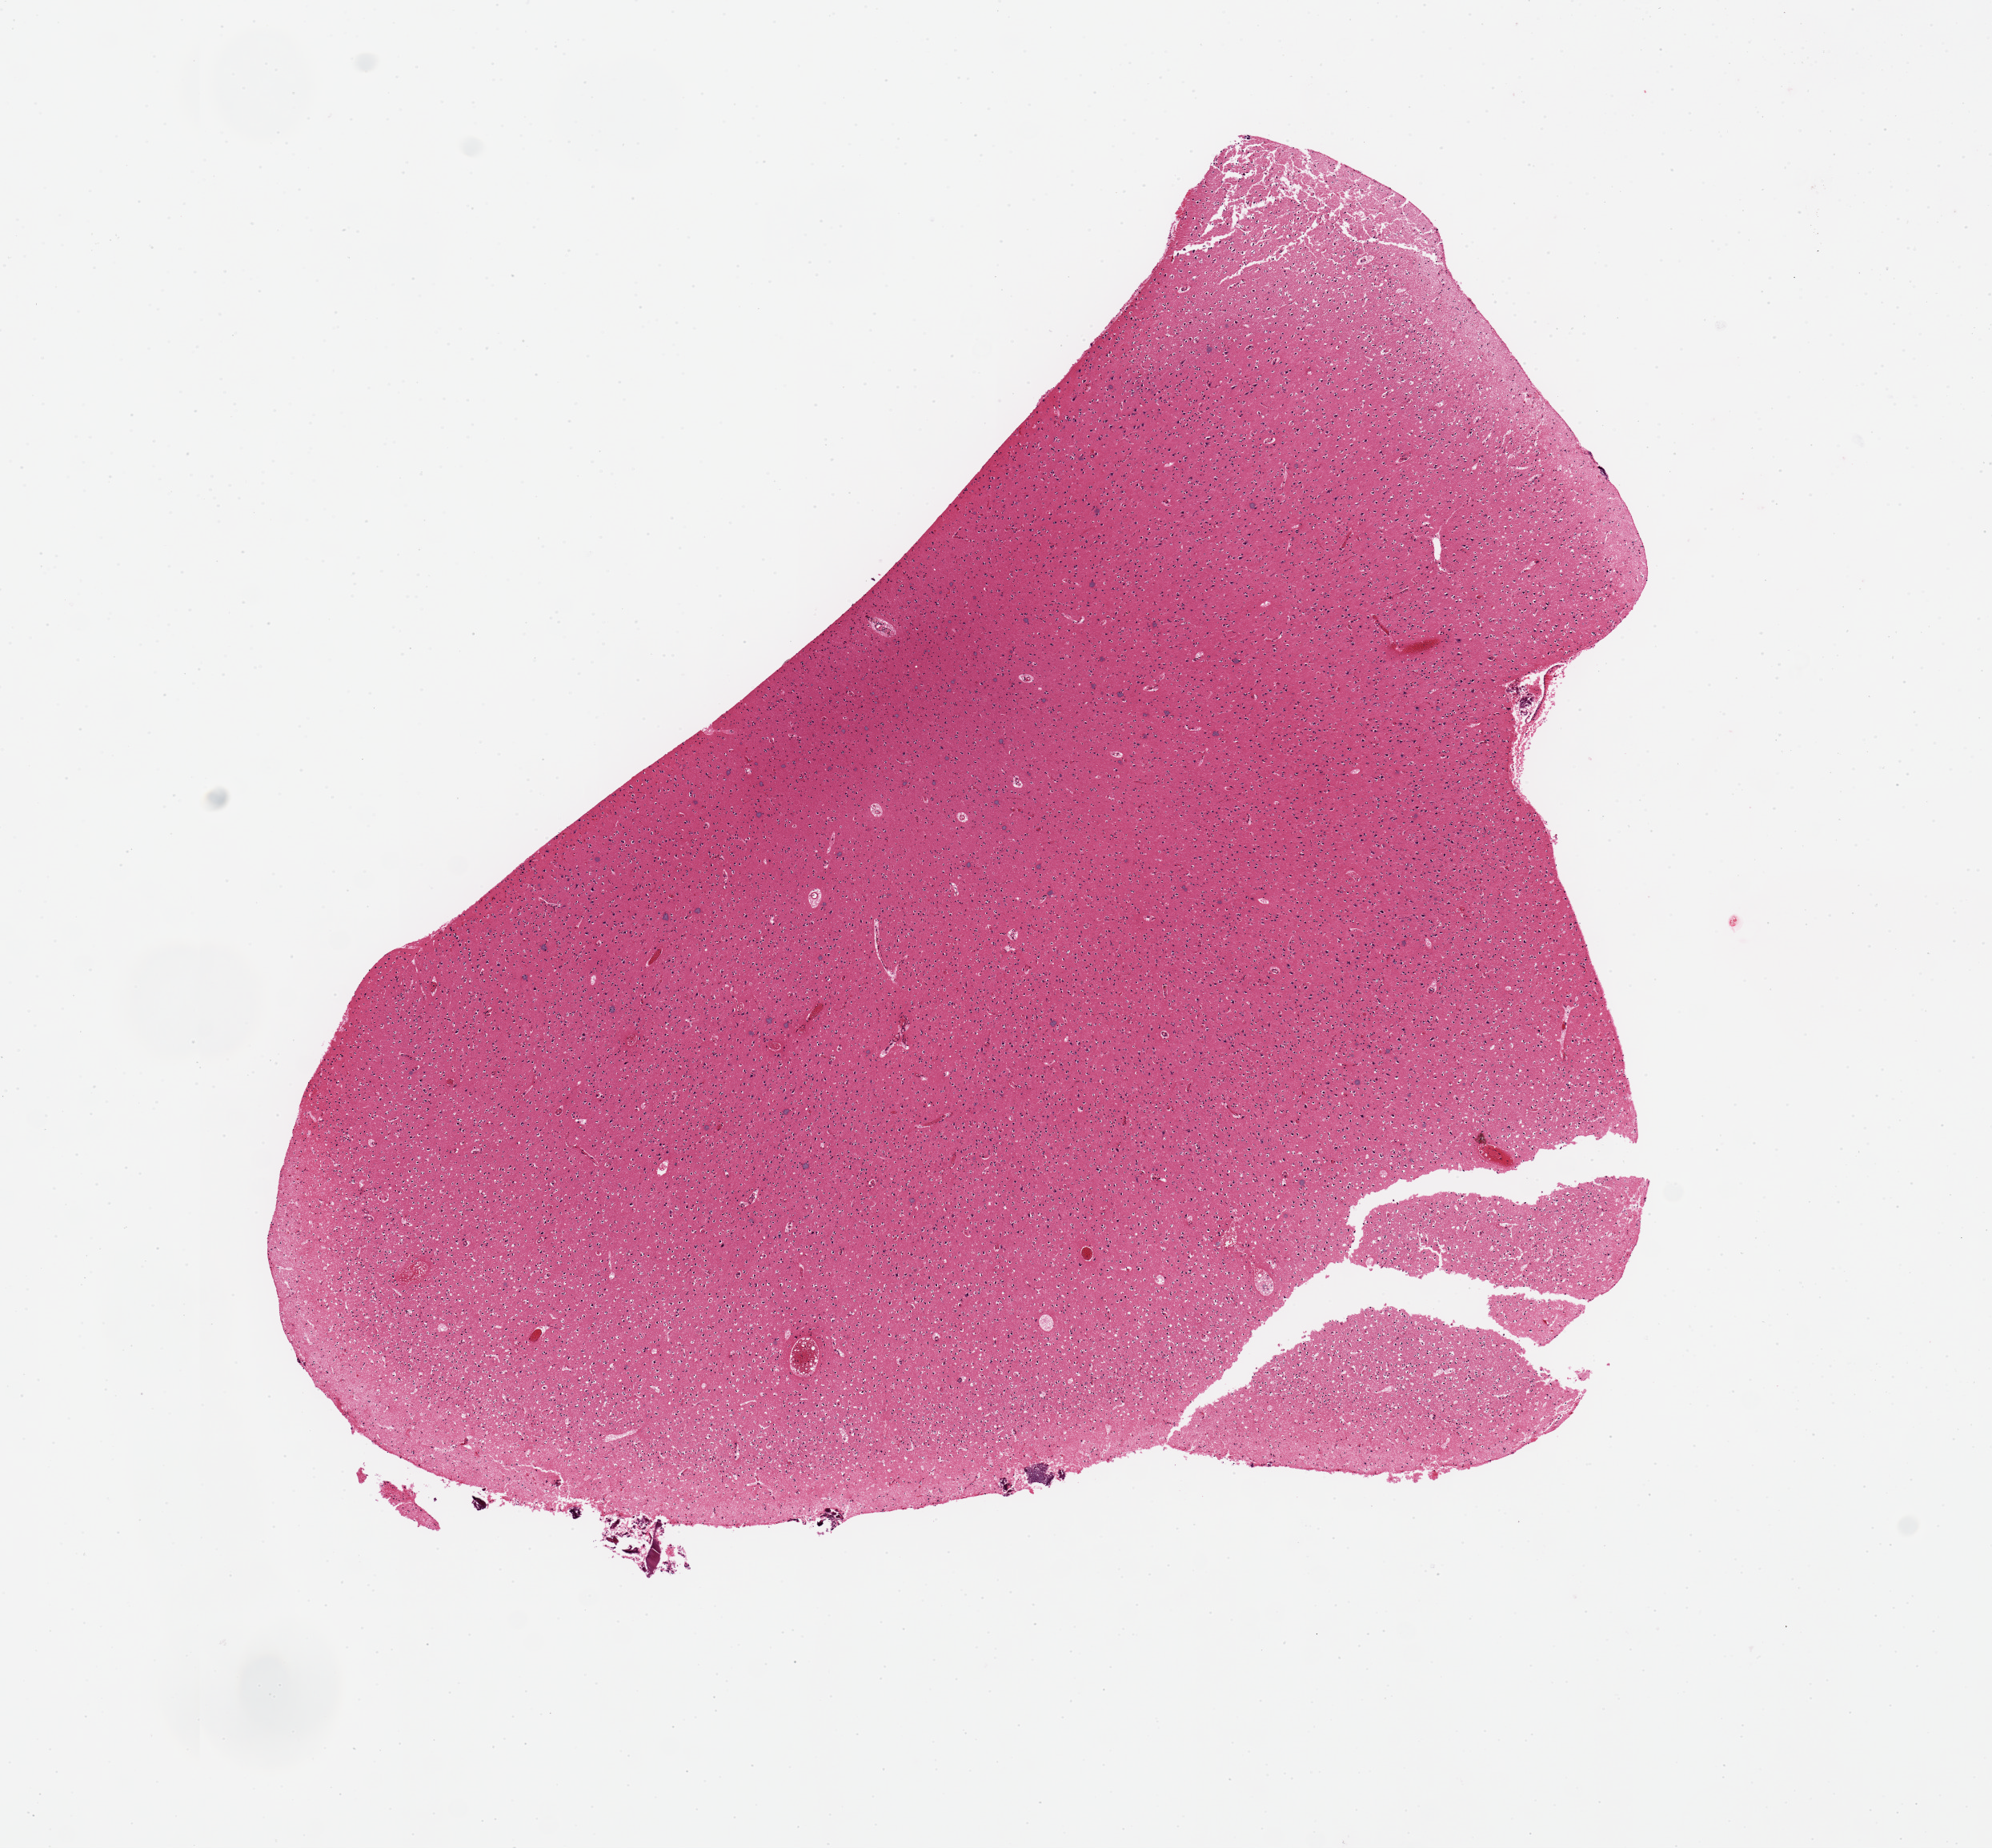
Whole-slide image, hematoxylin and eosin (H&E) stain, a low-resolution overview of the entire scanned area, about 9.8 x 9.1 mm. PAXgene-fixed paraffin-embedded (PFPE) section. Section of cerebral cortex (target tissue). Tissue donor sample. Donor: male.
Review note (as recorded): well preserved; 8x5 mm.